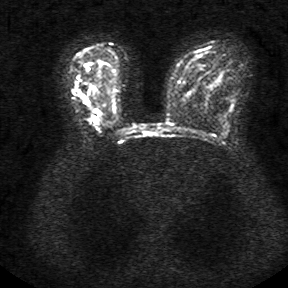
Breast MRI, one axial slice; position 21 of 34 along the scan axis; diffusion-weighted series; image 2 of 4 stored at this slice position (different b-values; order by instance number); 1.5 T; 288 × 288 image matrix. Female patient.
Outlined on this slice (expert manual segmentation):
- tumour on diffusion-weighted imaging: bounding box <75,85,95,104> (left, top, right, bottom; pixels)